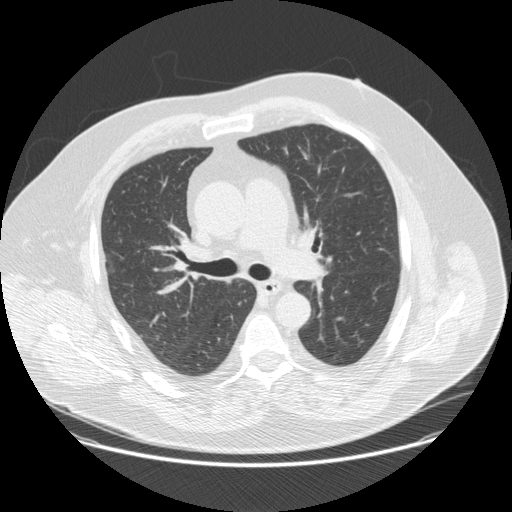
Axial slice from a low-dose chest CT screening exam; second annual screen; lung window (W 1500 / L -600 HU); standard (soft-tissue) reconstruction kernel (STANDARD); 512 × 512 image matrix. Male, age 69 years at enrolment. Former smoker at enrolment.
• Expert reader's lesion annotation, bounding box [x1, y1, x2, y2] px = [342, 328, 371, 354].
• No non-calcified nodule or mass ≥4 mm was recorded by the screening reader at this exam.
• Later outcome: lung cancer diagnosed 534 days after this screen (after the third annual screen) — squamous cell carcinoma, NOS, left lower lobe, moderately differentiated (G2), stage IA (AJCC 6th edition), 14 mm at pathology.